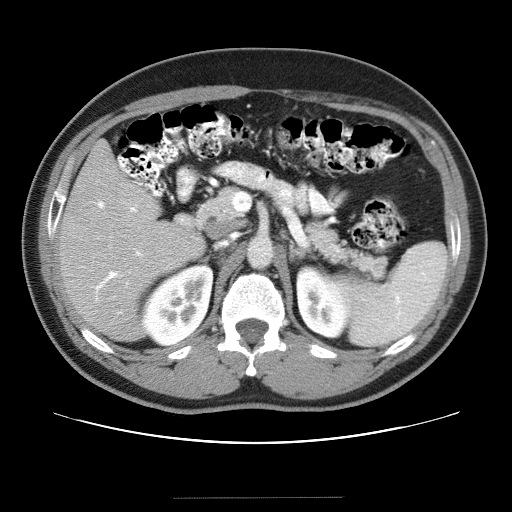
Contrast-enhanced abdominal CT (liver protocol), one axial slice. Position 15 of 40 along the scan axis. Reconstruction kernel STANDARD. Soft-tissue window (W 400 / L 40 HU). 5 mm slice thickness. 512 × 512 image matrix. From the clinical record (not read from this slice): diagnosis: hepatocellular carcinoma (patient treated with transarterial chemoembolisation; whether this scan precedes or follows treatment is not stated here); TNM stage (as recorded): Stage-IVA; Child-Pugh class: B.
Outlined on this slice (semi-automatic segmentation, software-assisted and operator-edited):
- liver parenchyma outside the tumour (the mass and vessels are separate outlines, so this box may not span the whole liver): bounding box <58,140,204,340> (left, top, right, bottom; pixels)
- liver vessels: <81,201,199,315>